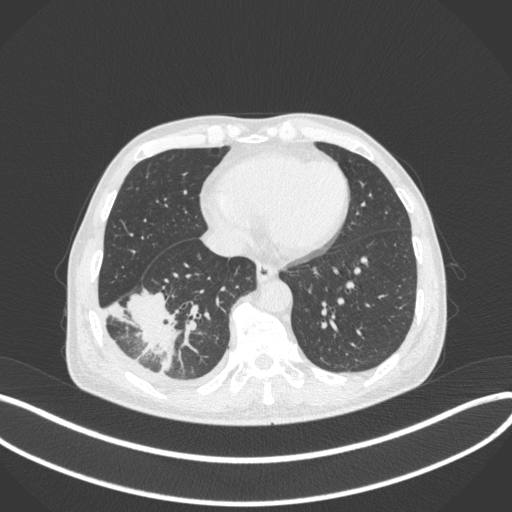
Chest CT, one axial slice. Position 120 of 385 along the scan axis. Lung window (W 1500 / L -600 HU). 1 mm slice thickness. 512 × 512 image matrix, field of view 400 × 400 mm. Male patient, age 64 years. Case-level facts recorded for this patient, not image findings: clinical TNM (as recorded): T3 N0 M0.
Structures marked on this image (rectangle marked by the reading radiologist):
- lung tumour (recorded histology: adenocarcinoma): bounding box (x1, y1, x2, y2) in pixels: (123, 286, 180, 375)